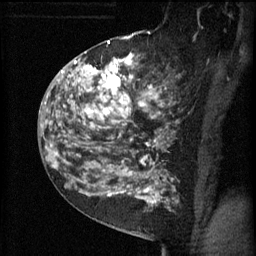
Breast MRI (dynamic contrast-enhanced), one sagittal slice; position 34 of 60 along the scan axis; 3 images stored at this slice position (order not interpretable as contrast timing); 1.5 T; TE 4.2 ms, TR 11 ms; 2 mm slice thickness; 256 × 256 image matrix, field of view 180 × 180 mm. Patient: female, 52 years.
Annotated regions visible in this slice (semi-automatically segmented with operator editing):
- analysis volume of interest (the breast-tissue region the enhancement analysis was run in; not a lesion): bounding box [x1, y1, x2, y2] px = [81, 52, 174, 157]
- tumour enhancement mask (voxels above the 70 % enhancement threshold inside the analysis volume of interest): [81, 54, 163, 157]